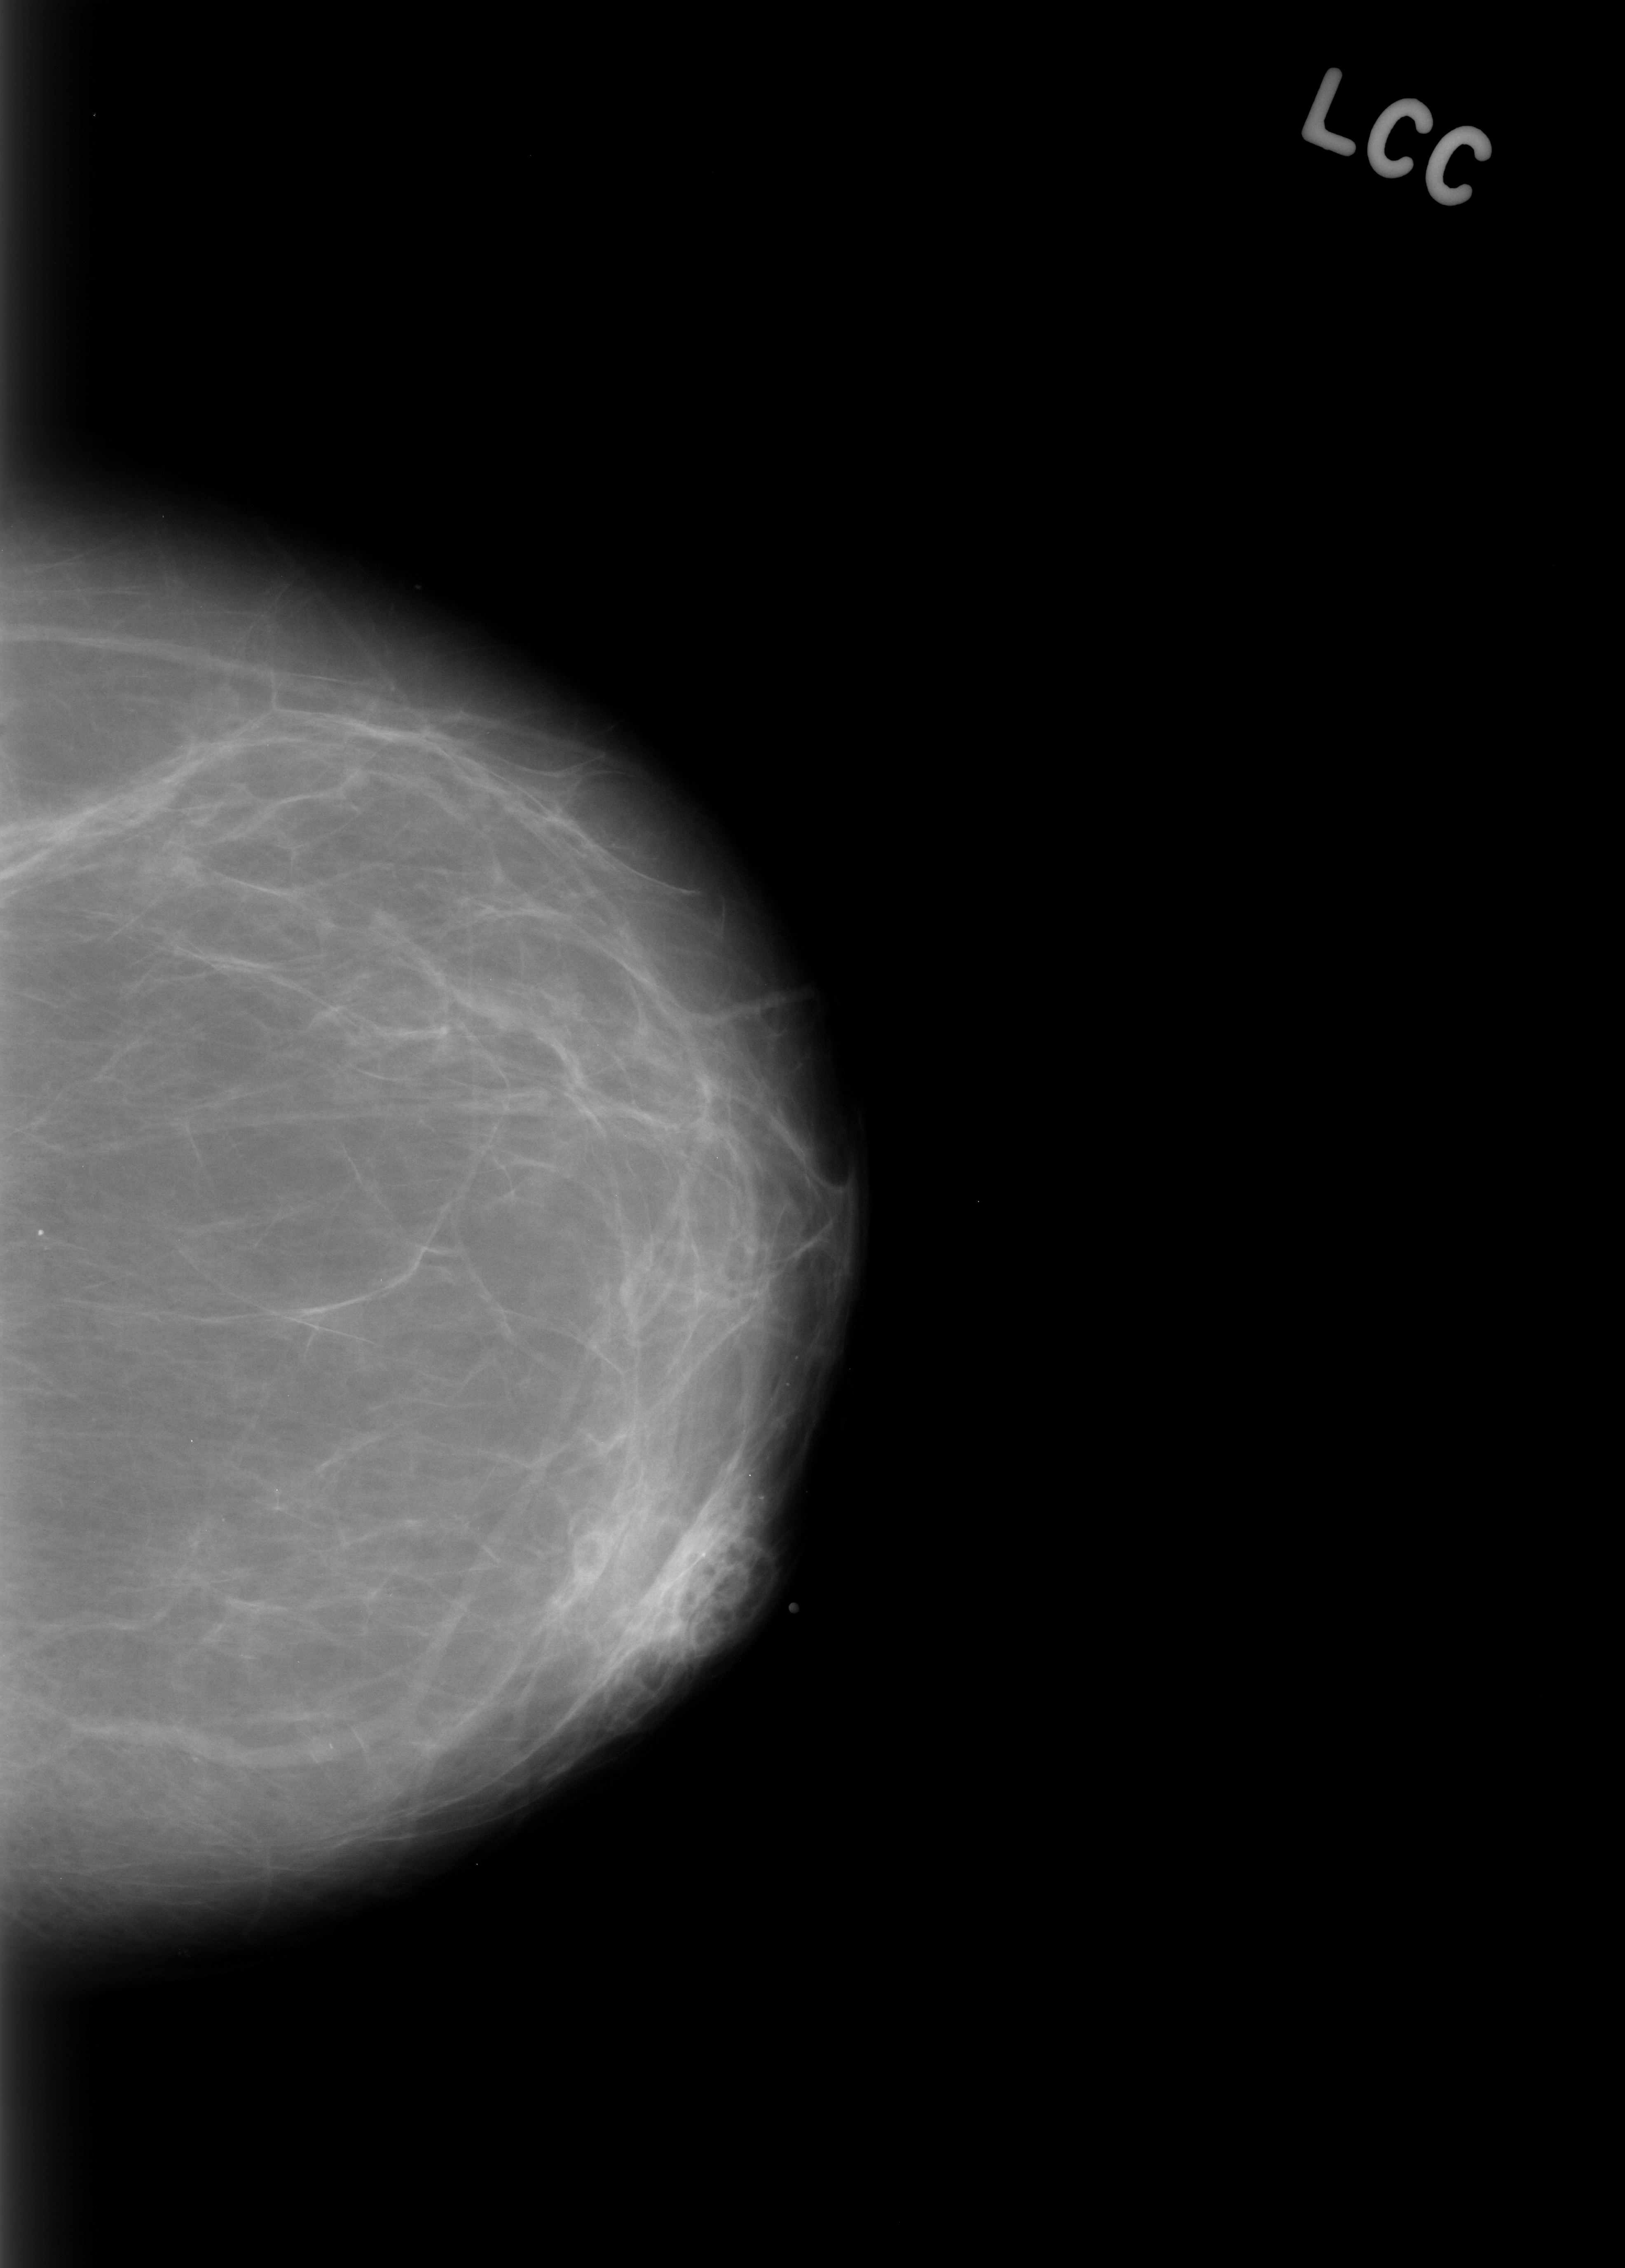
Mammogram (digitized film); left breast; craniocaudal (CC) view; breast composition: almost entirely fatty (BI-RADS density category 1 of 4); 1625 × 2268 image matrix.
Expert-marked regions of interest on this image (one box per marked abnormality):
- mass, shape focal asymmetric density, margins ill defined; BI-RADS assessment category 3; subtlety rating 5 on a 1 (subtle) to 5 (obvious) scale; pathology (as recorded): benign: bounding box [x1, y1, x2, y2] px = [608, 1524, 774, 1698]